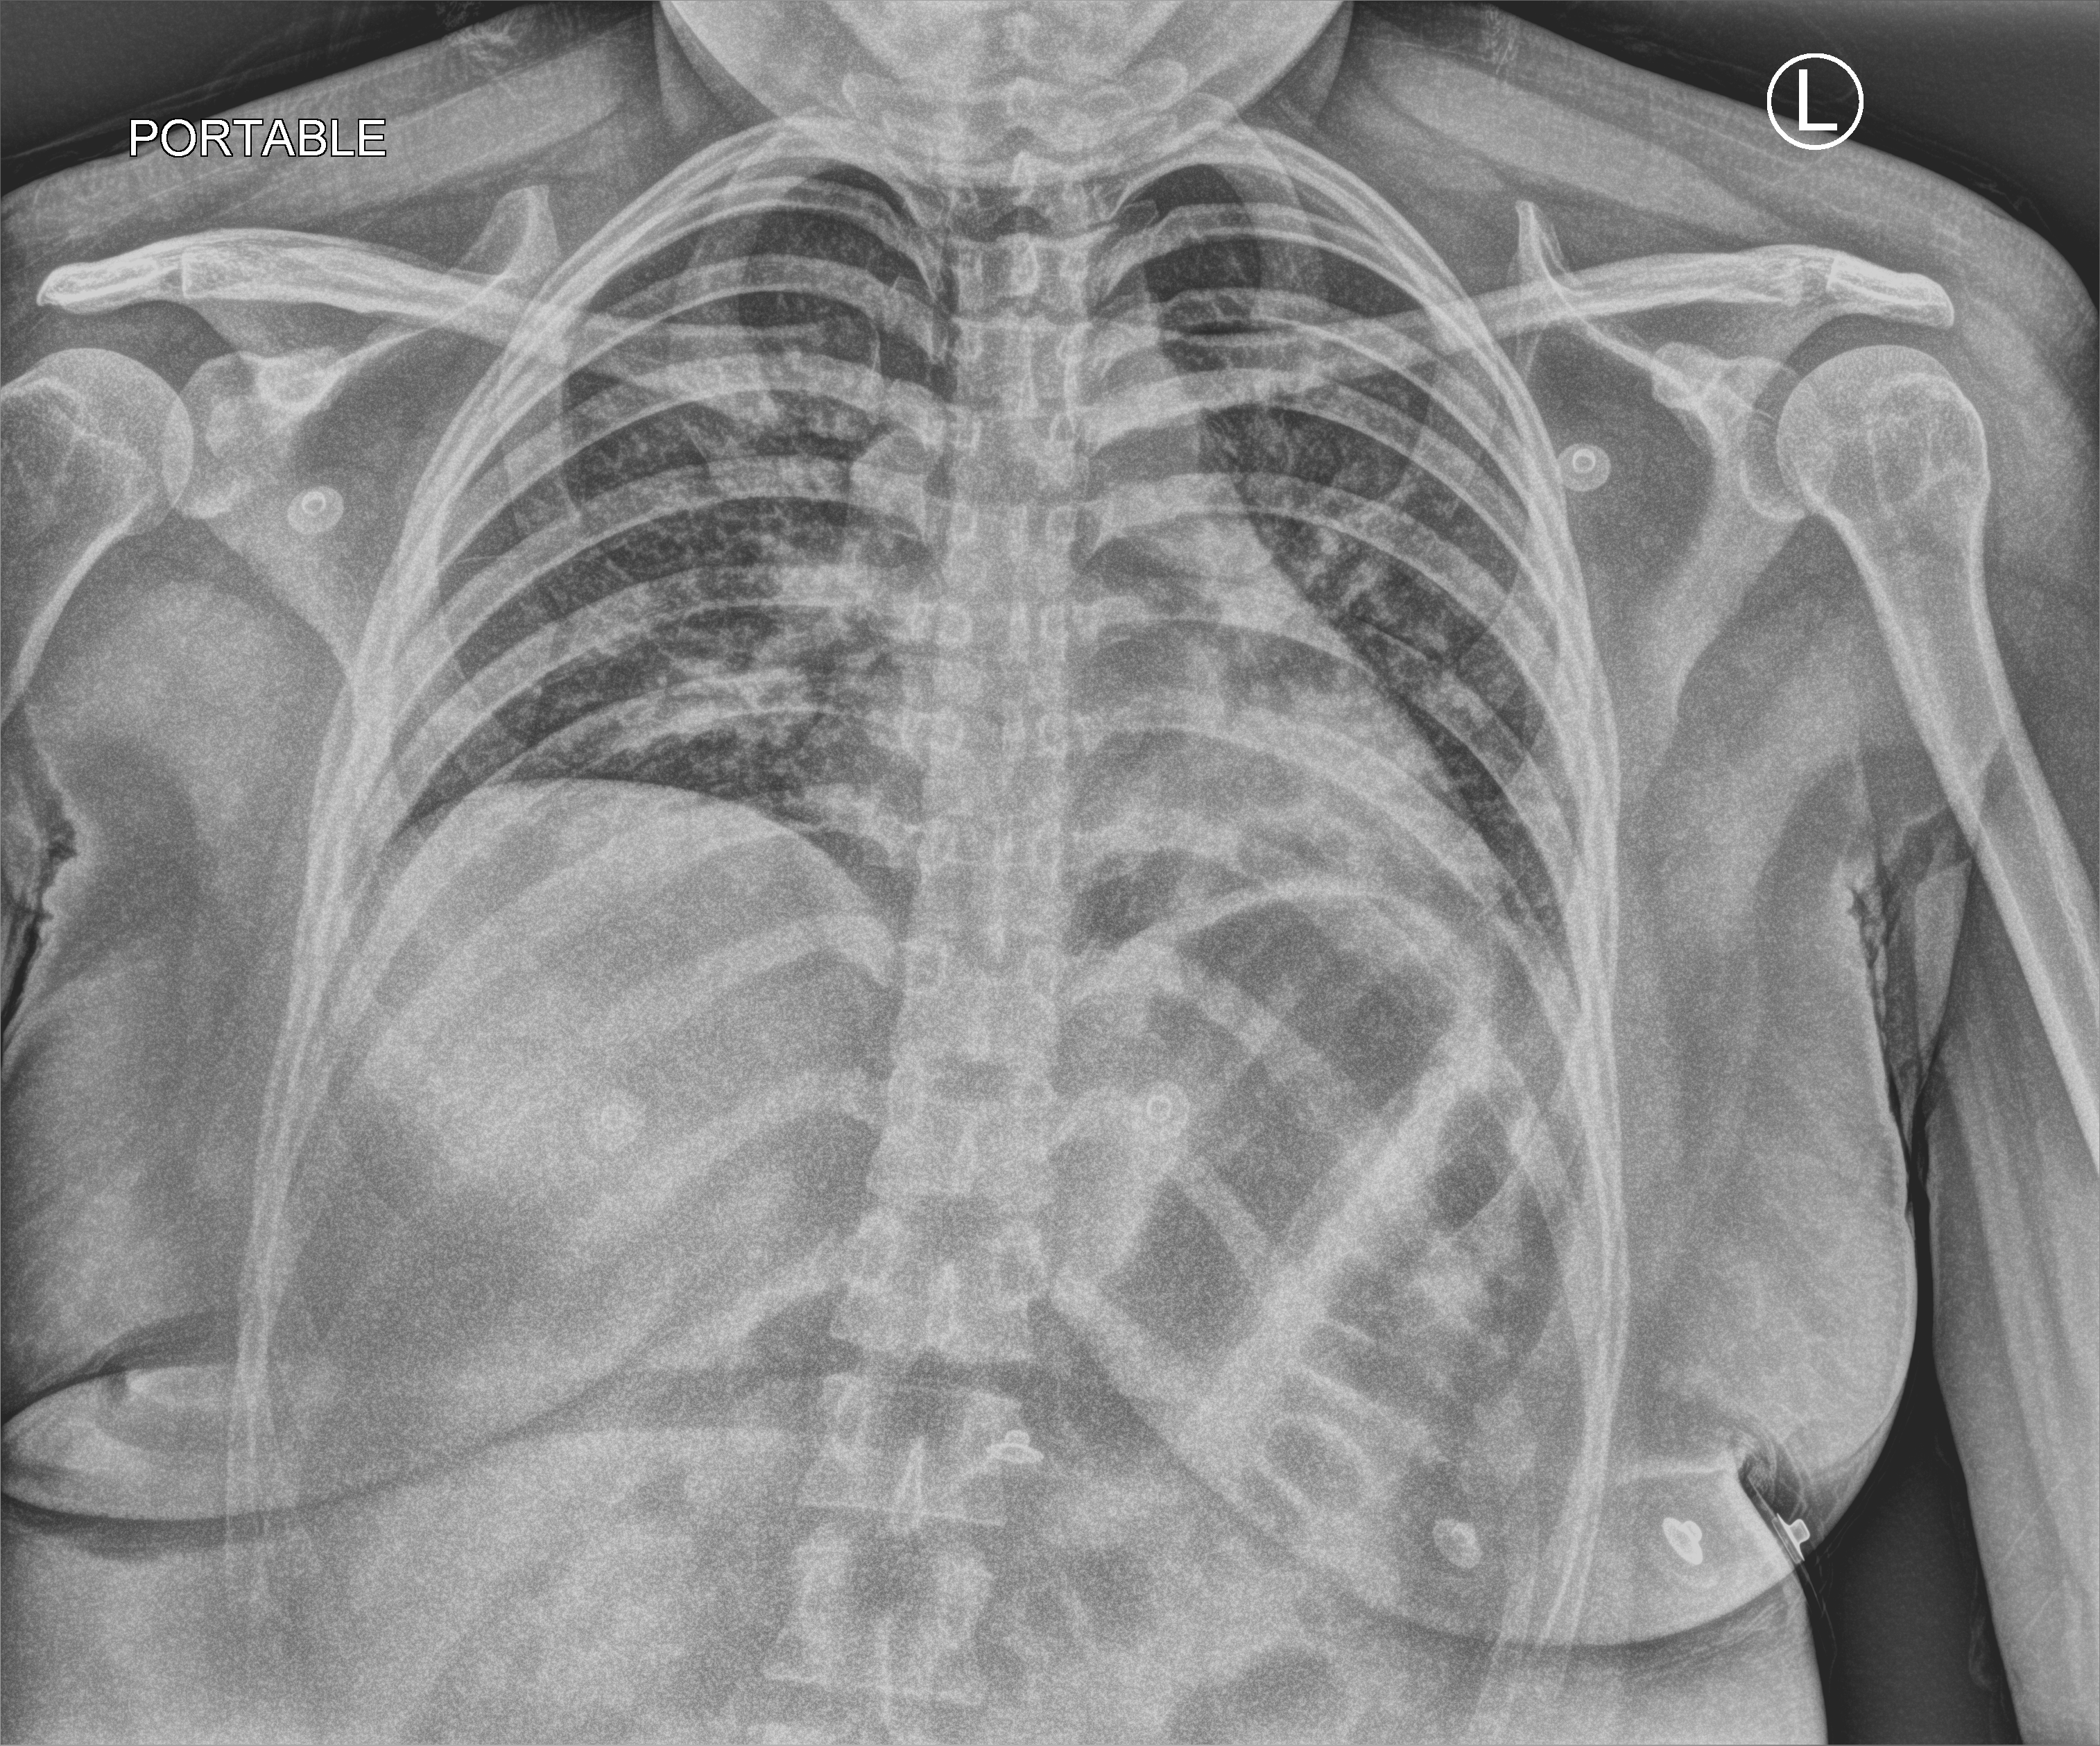
Chest X-ray (portable), anteroposterior (AP) projection. Female patient hospitalised with COVID-19, age 18–59 years.
Hospital-stay facts (about this admission, not read from this image; timing relative to this image not recorded):
- smoking status (admission record): never
- admitted to intensive care during this hospital stay: no
- hypertension (admission record): no